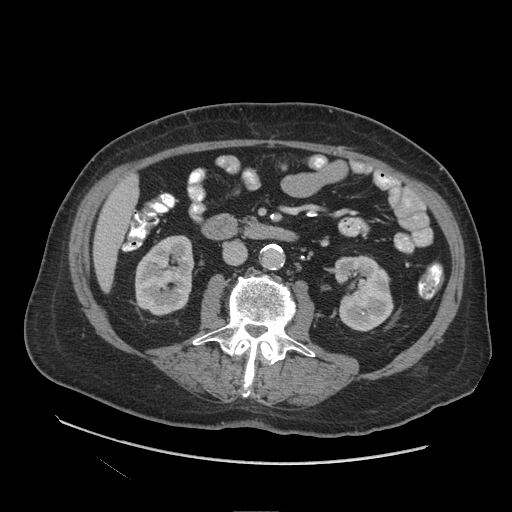
Contrast-enhanced abdominal CT (liver protocol), one axial slice. Soft-tissue window (W 400 / L 40 HU). 2.5 mm slice thickness. 512 × 512 image matrix. Case-level facts recorded for this patient, not image findings: diagnosis: hepatocellular carcinoma (patient treated with transarterial chemoembolisation; whether this scan precedes or follows treatment is not stated here); TNM stage (as recorded): Stage-I; Child-Pugh class: A.
Outlined on this slice (semi-automatic segmentation, software-assisted and operator-edited):
- liver parenchyma outside the tumour (the mass and vessels are separate outlines, so this box may not span the whole liver): box from (x=94, y=174) to (x=138, y=292) px